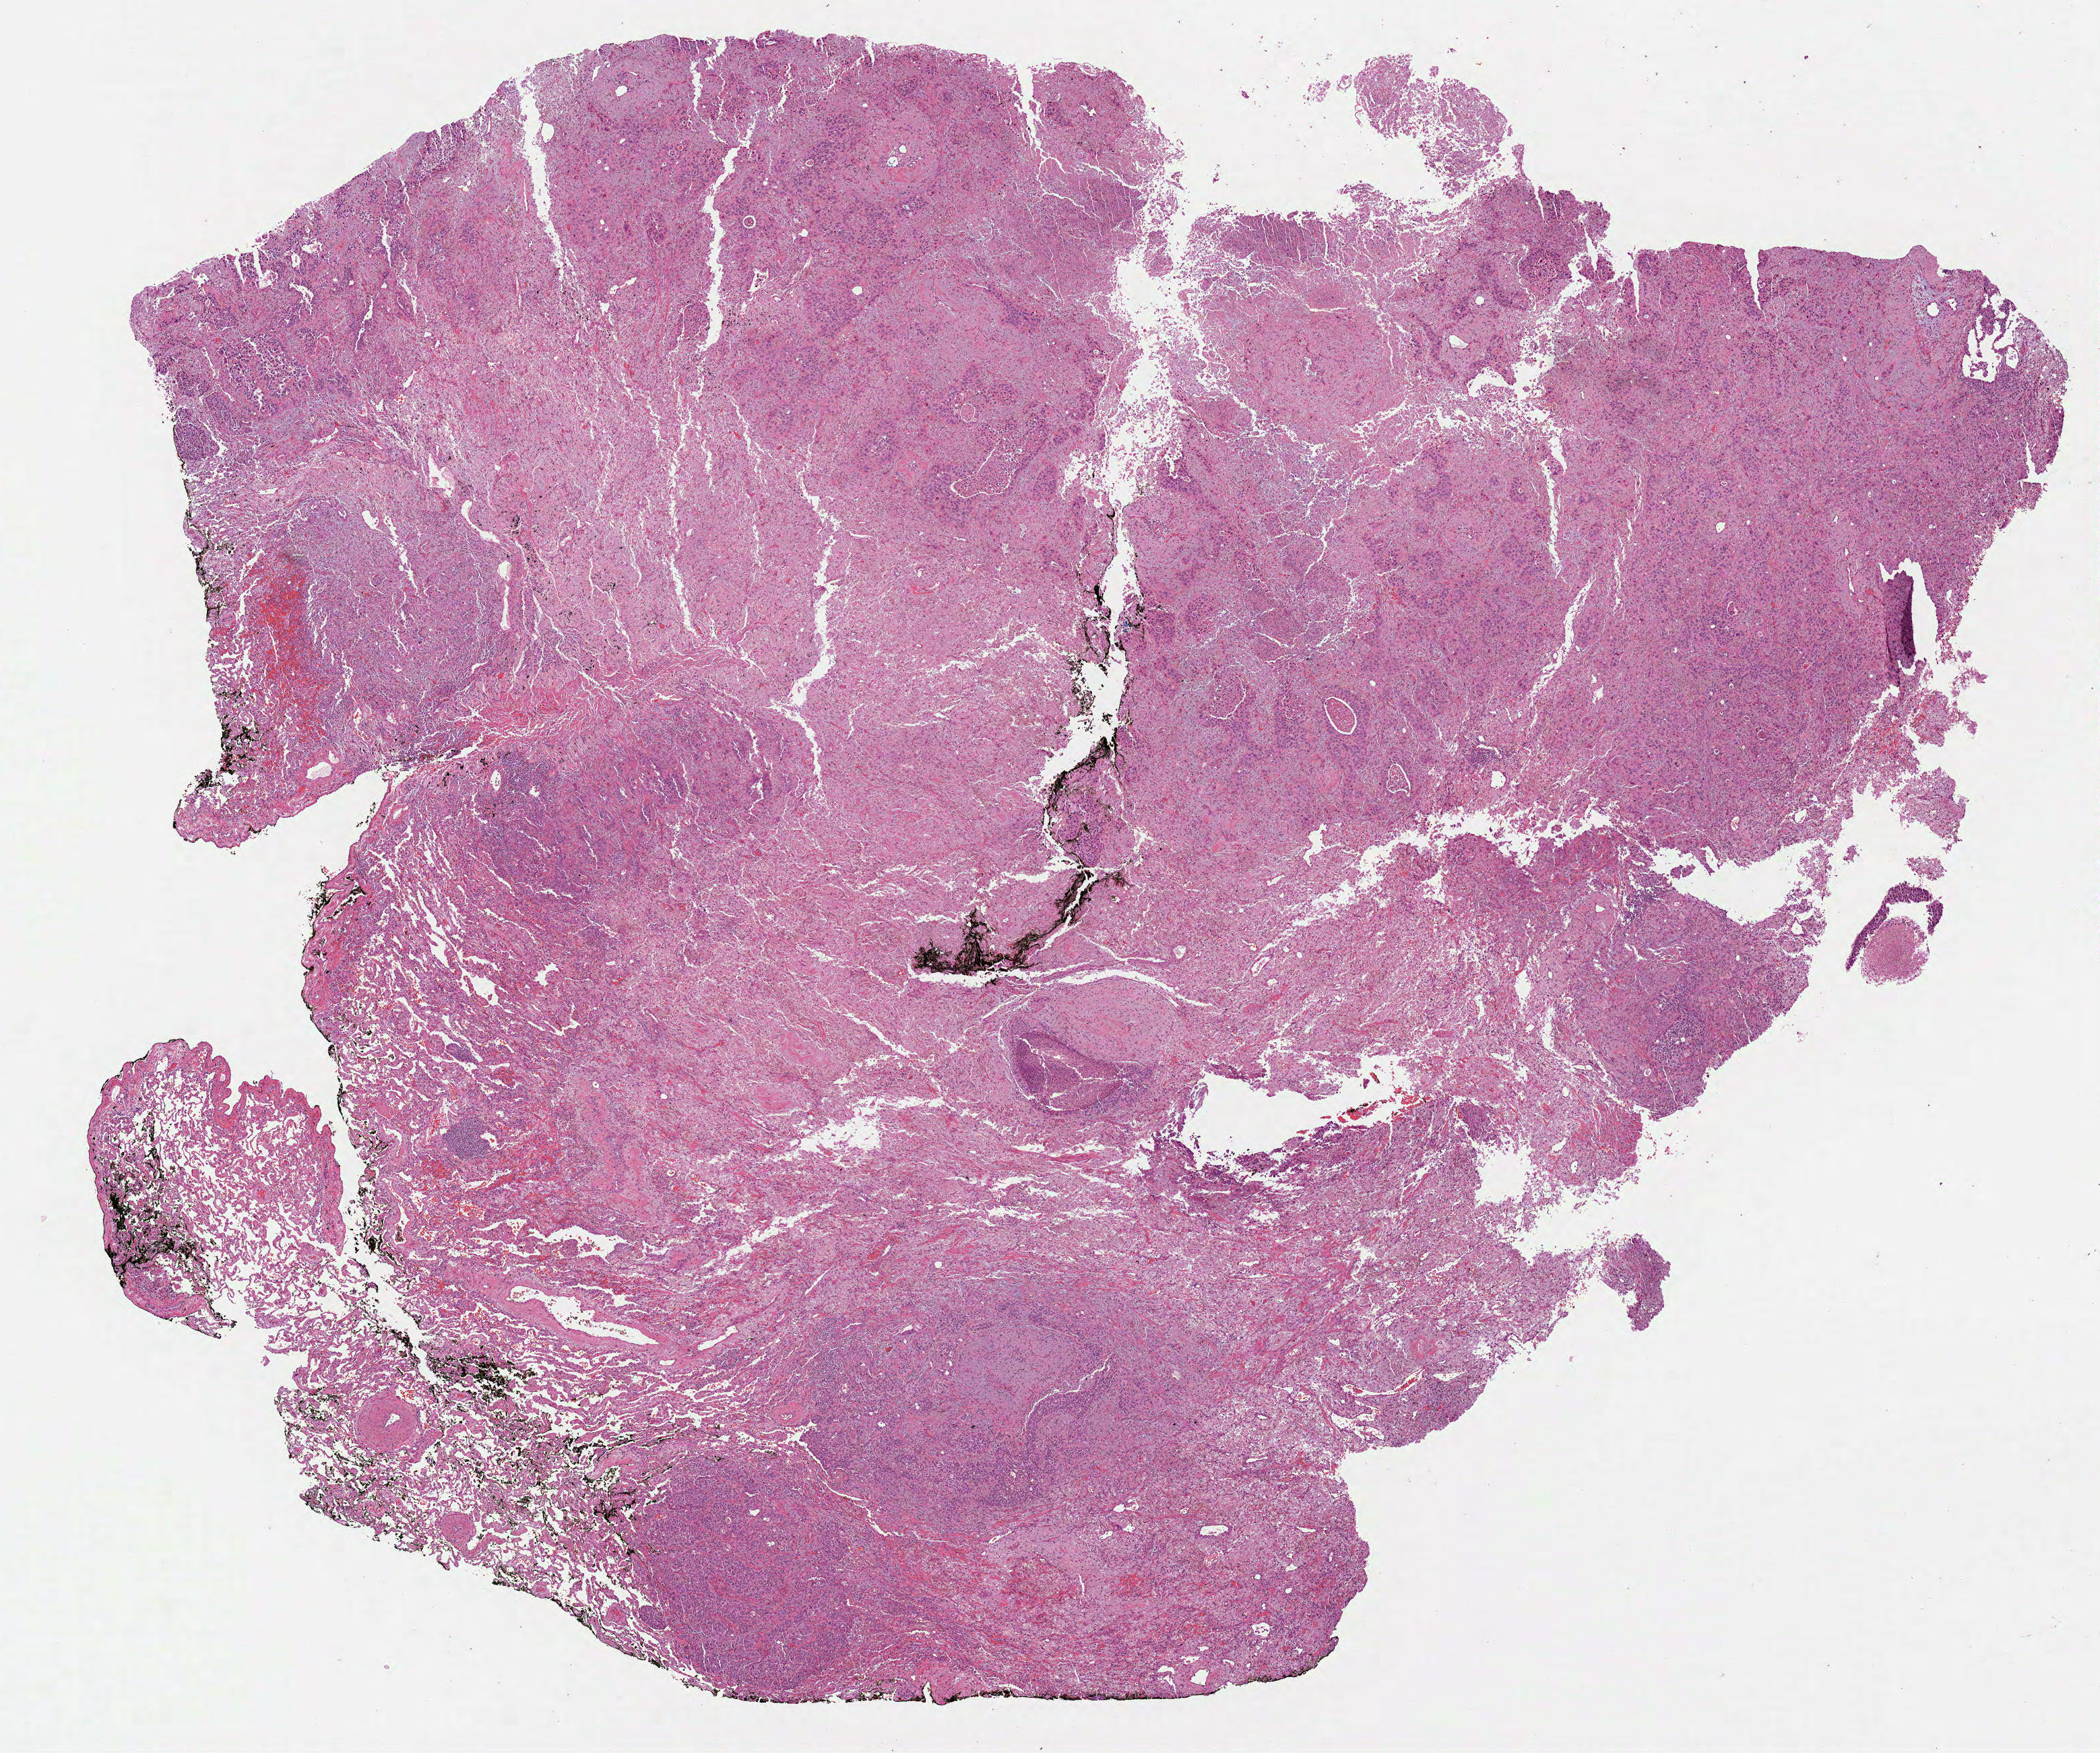
Whole-slide histology image, H&E, shown as a low-resolution overview of the whole scanned area (about 12.6 x 10.5 mm), formalin-fixed paraffin-embedded (FFPE) diagnostic section, primary tumour sample from the lung. Male patient; age at initial diagnosis 76 years.
Laterality: left. TNM: T2a N0 MX. AJCC pathologic stage: IB (7th edition). Pathologic diagnosis: Adenocarcinoma, NOS (upper lobe, lung).